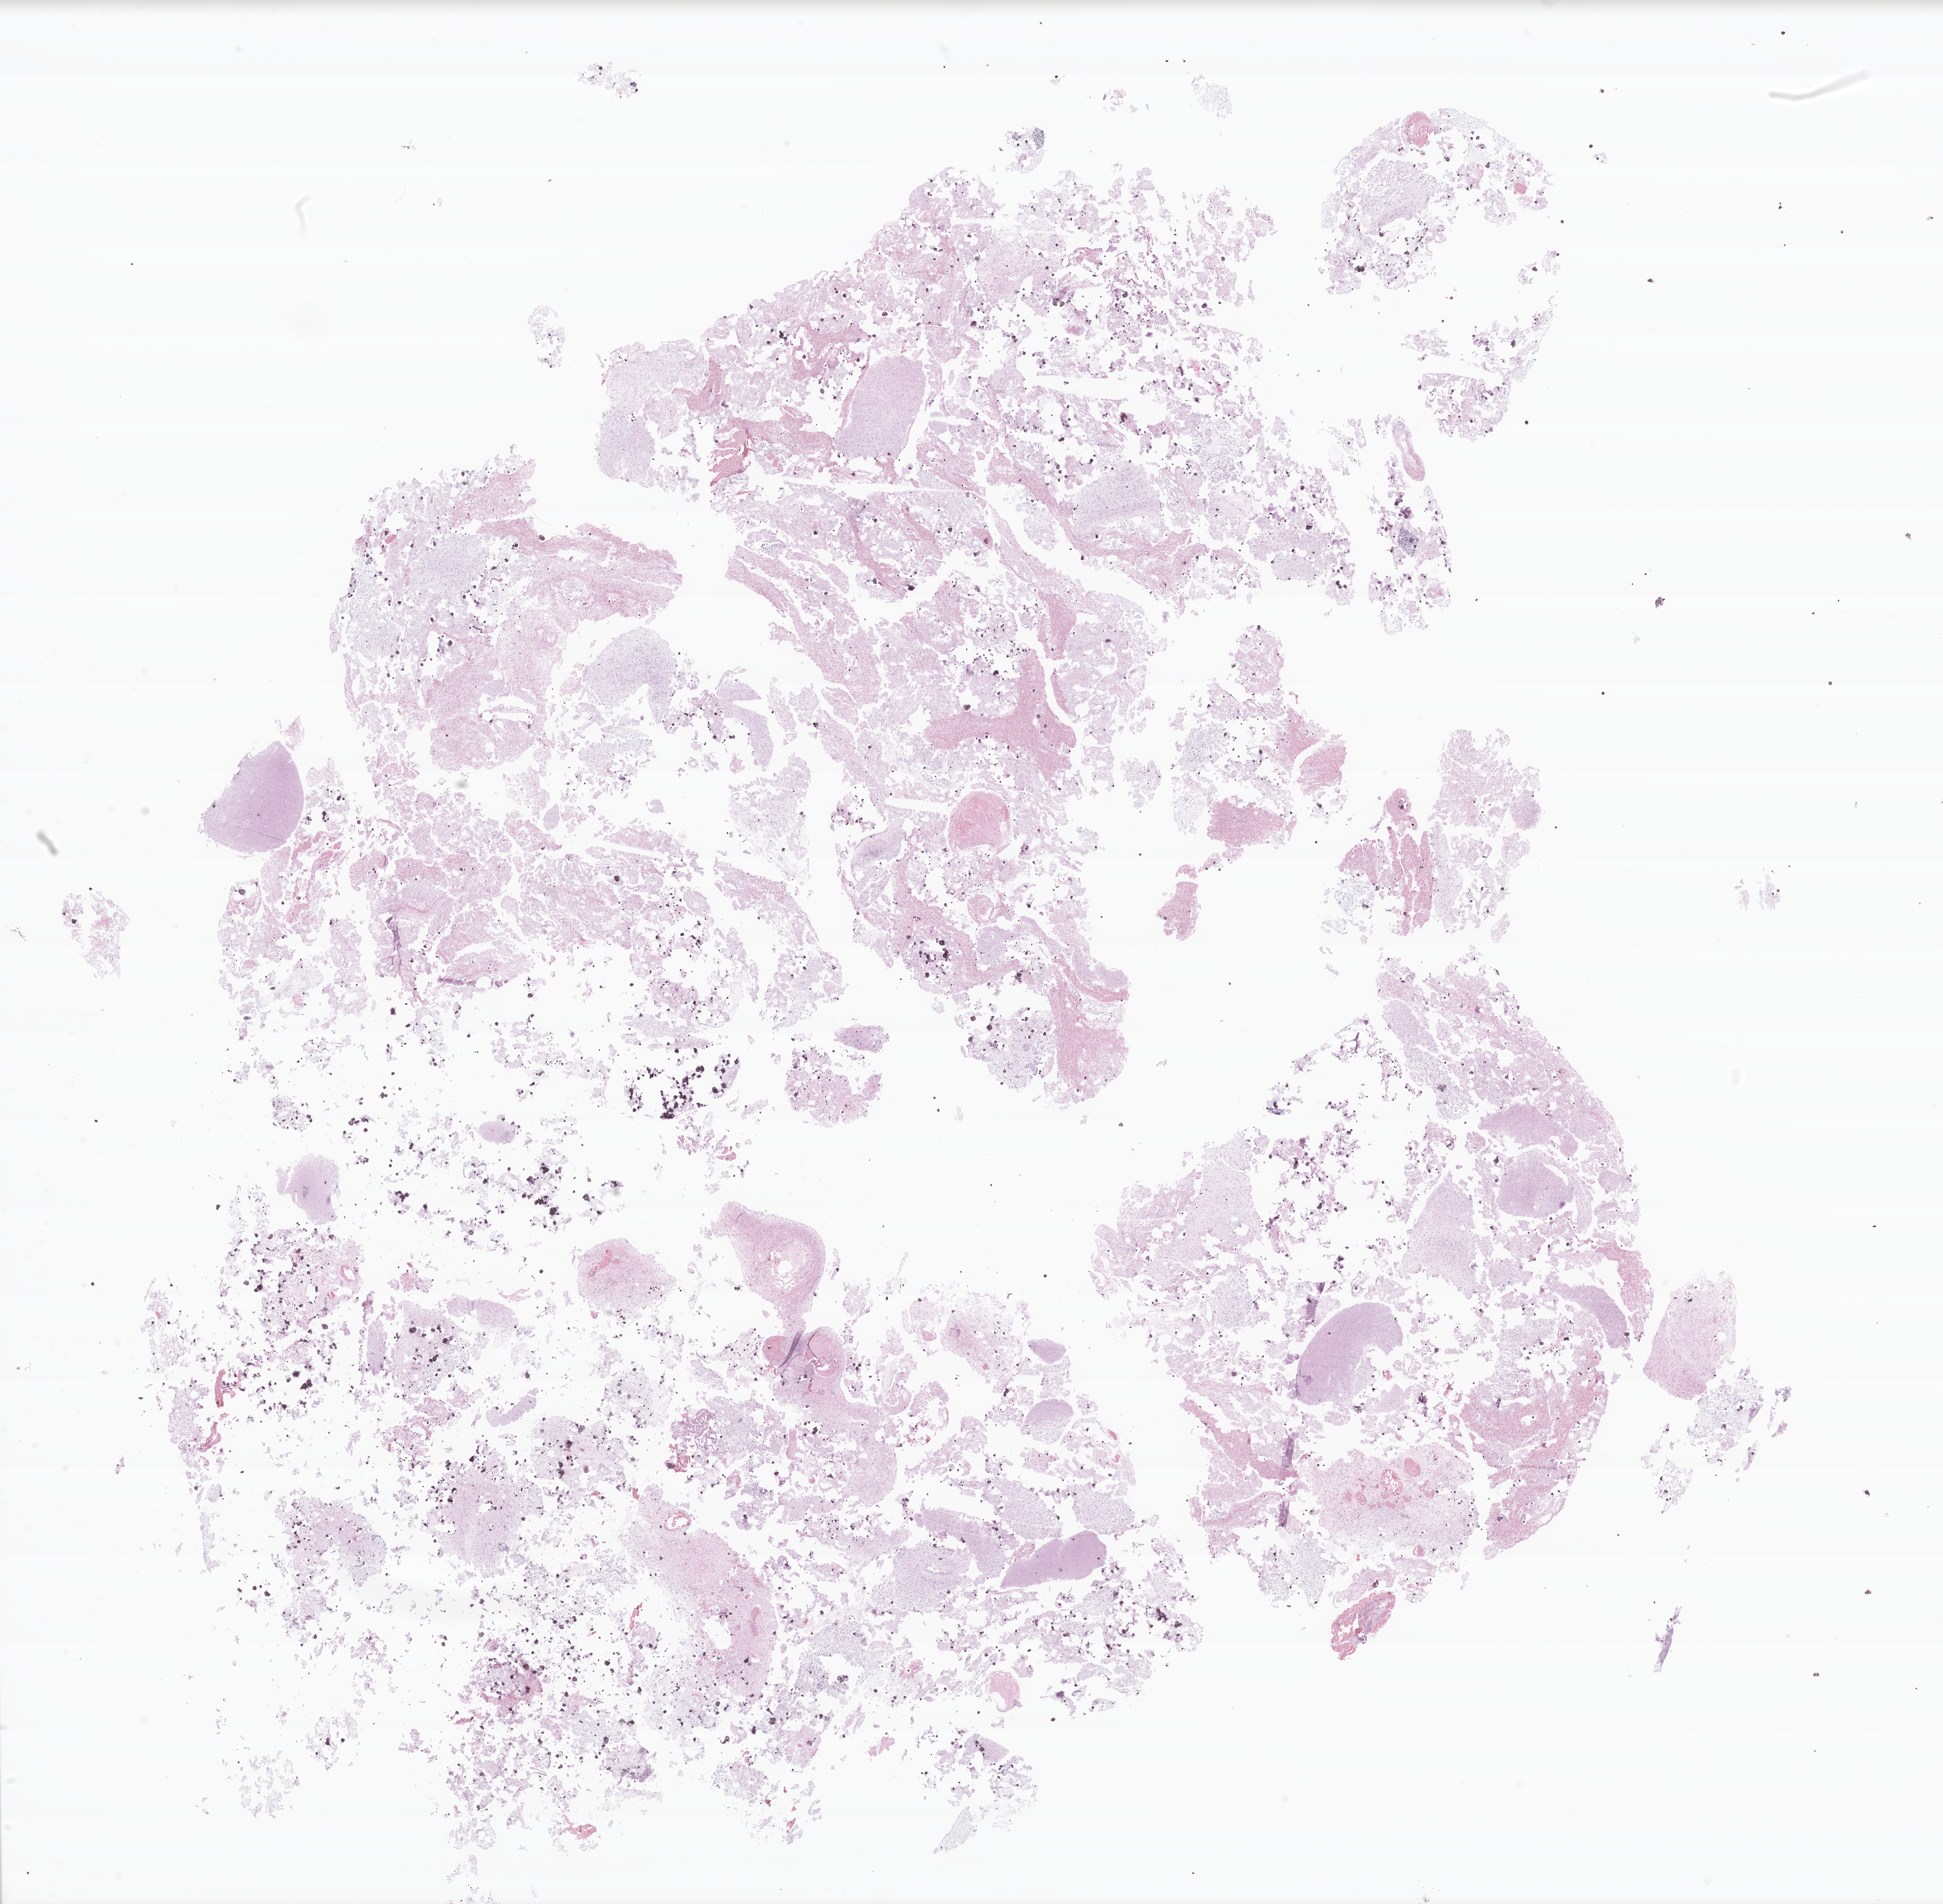
Digitized H&E-stained section of tumor tissue from the cerebellum, whole scanned area (about 23.7 x 23.3 mm) shown as a low-resolution overview. FFPE section. Patient: female, age 226 months (18 years 10 months).
Diagnosis (ICD-O-3 morphology term): Pilocytic astrocytoma.